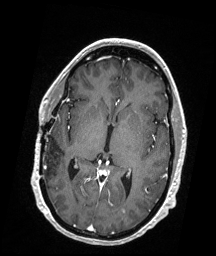
Brain MRI from a brain-tumour surgery series, one axial slice; position 94 of 176 along the scan axis; T1-weighted post-contrast; 1 mm slice thickness; 216 × 256 image matrix, field of view 211 × 250 mm. Case-level facts recorded for this patient, not image findings: histopathology: Demyelinating Lesions (Multiple Sclerosis Plaques); tumour location: Left Occipital.
Structures marked on this image (outlined manually by an expert reader):
- tumour: bounding box [x1, y1, x2, y2] px = [120, 208, 127, 214]